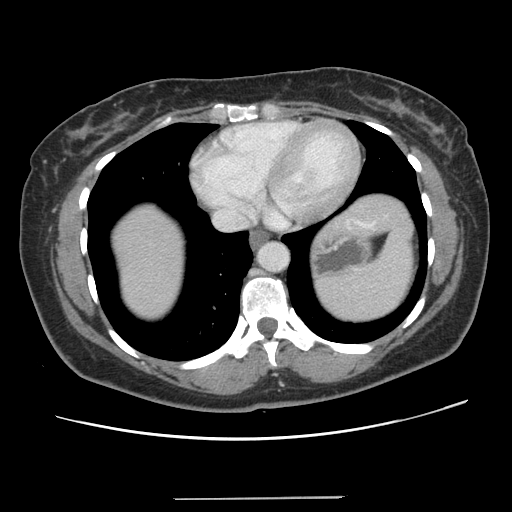
Contrast-enhanced abdominal CT, one axial slice; position 124 of 141 along the scan axis; 120 kVp; intravenous contrast given; soft-tissue window (W 400 / L 40 HU); 2.5 mm slice thickness; 512 × 512 image matrix, field of view 366 × 366 mm. Female patient, age 53 years. Case-level facts recorded for this patient, not image findings: diagnosis: colorectal cancer liver metastases, imaged before liver resection; multiple liver metastases: no.
Outlined on this slice (expert manual segmentation):
- liver: bounding box (x1, y1, x2, y2) in pixels: (110, 194, 406, 320)
- planned liver remnant (the part of the liver to remain after resection): (111, 215, 185, 321)